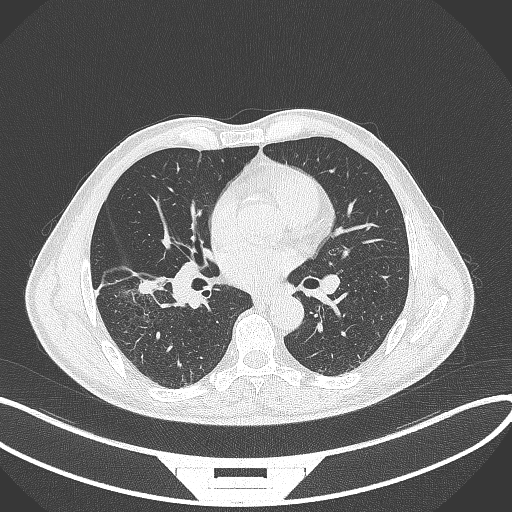
Chest CT, one axial slice. Slice 176 of 364 in the series (ordered by position). Reconstruction kernel B70f. Lung window (W 1500 / L -600 HU). 512 × 512 image matrix, field of view 400 × 400 mm. Male patient, age 58 years. From the clinical record (not read from this slice): clinical TNM (as recorded): T3 N0 M0.
Structures marked on this image (bounding box drawn by a radiologist):
- lung tumour (recorded histology: squamous cell carcinoma): bounding box [x1, y1, x2, y2] px = [130, 278, 169, 297]